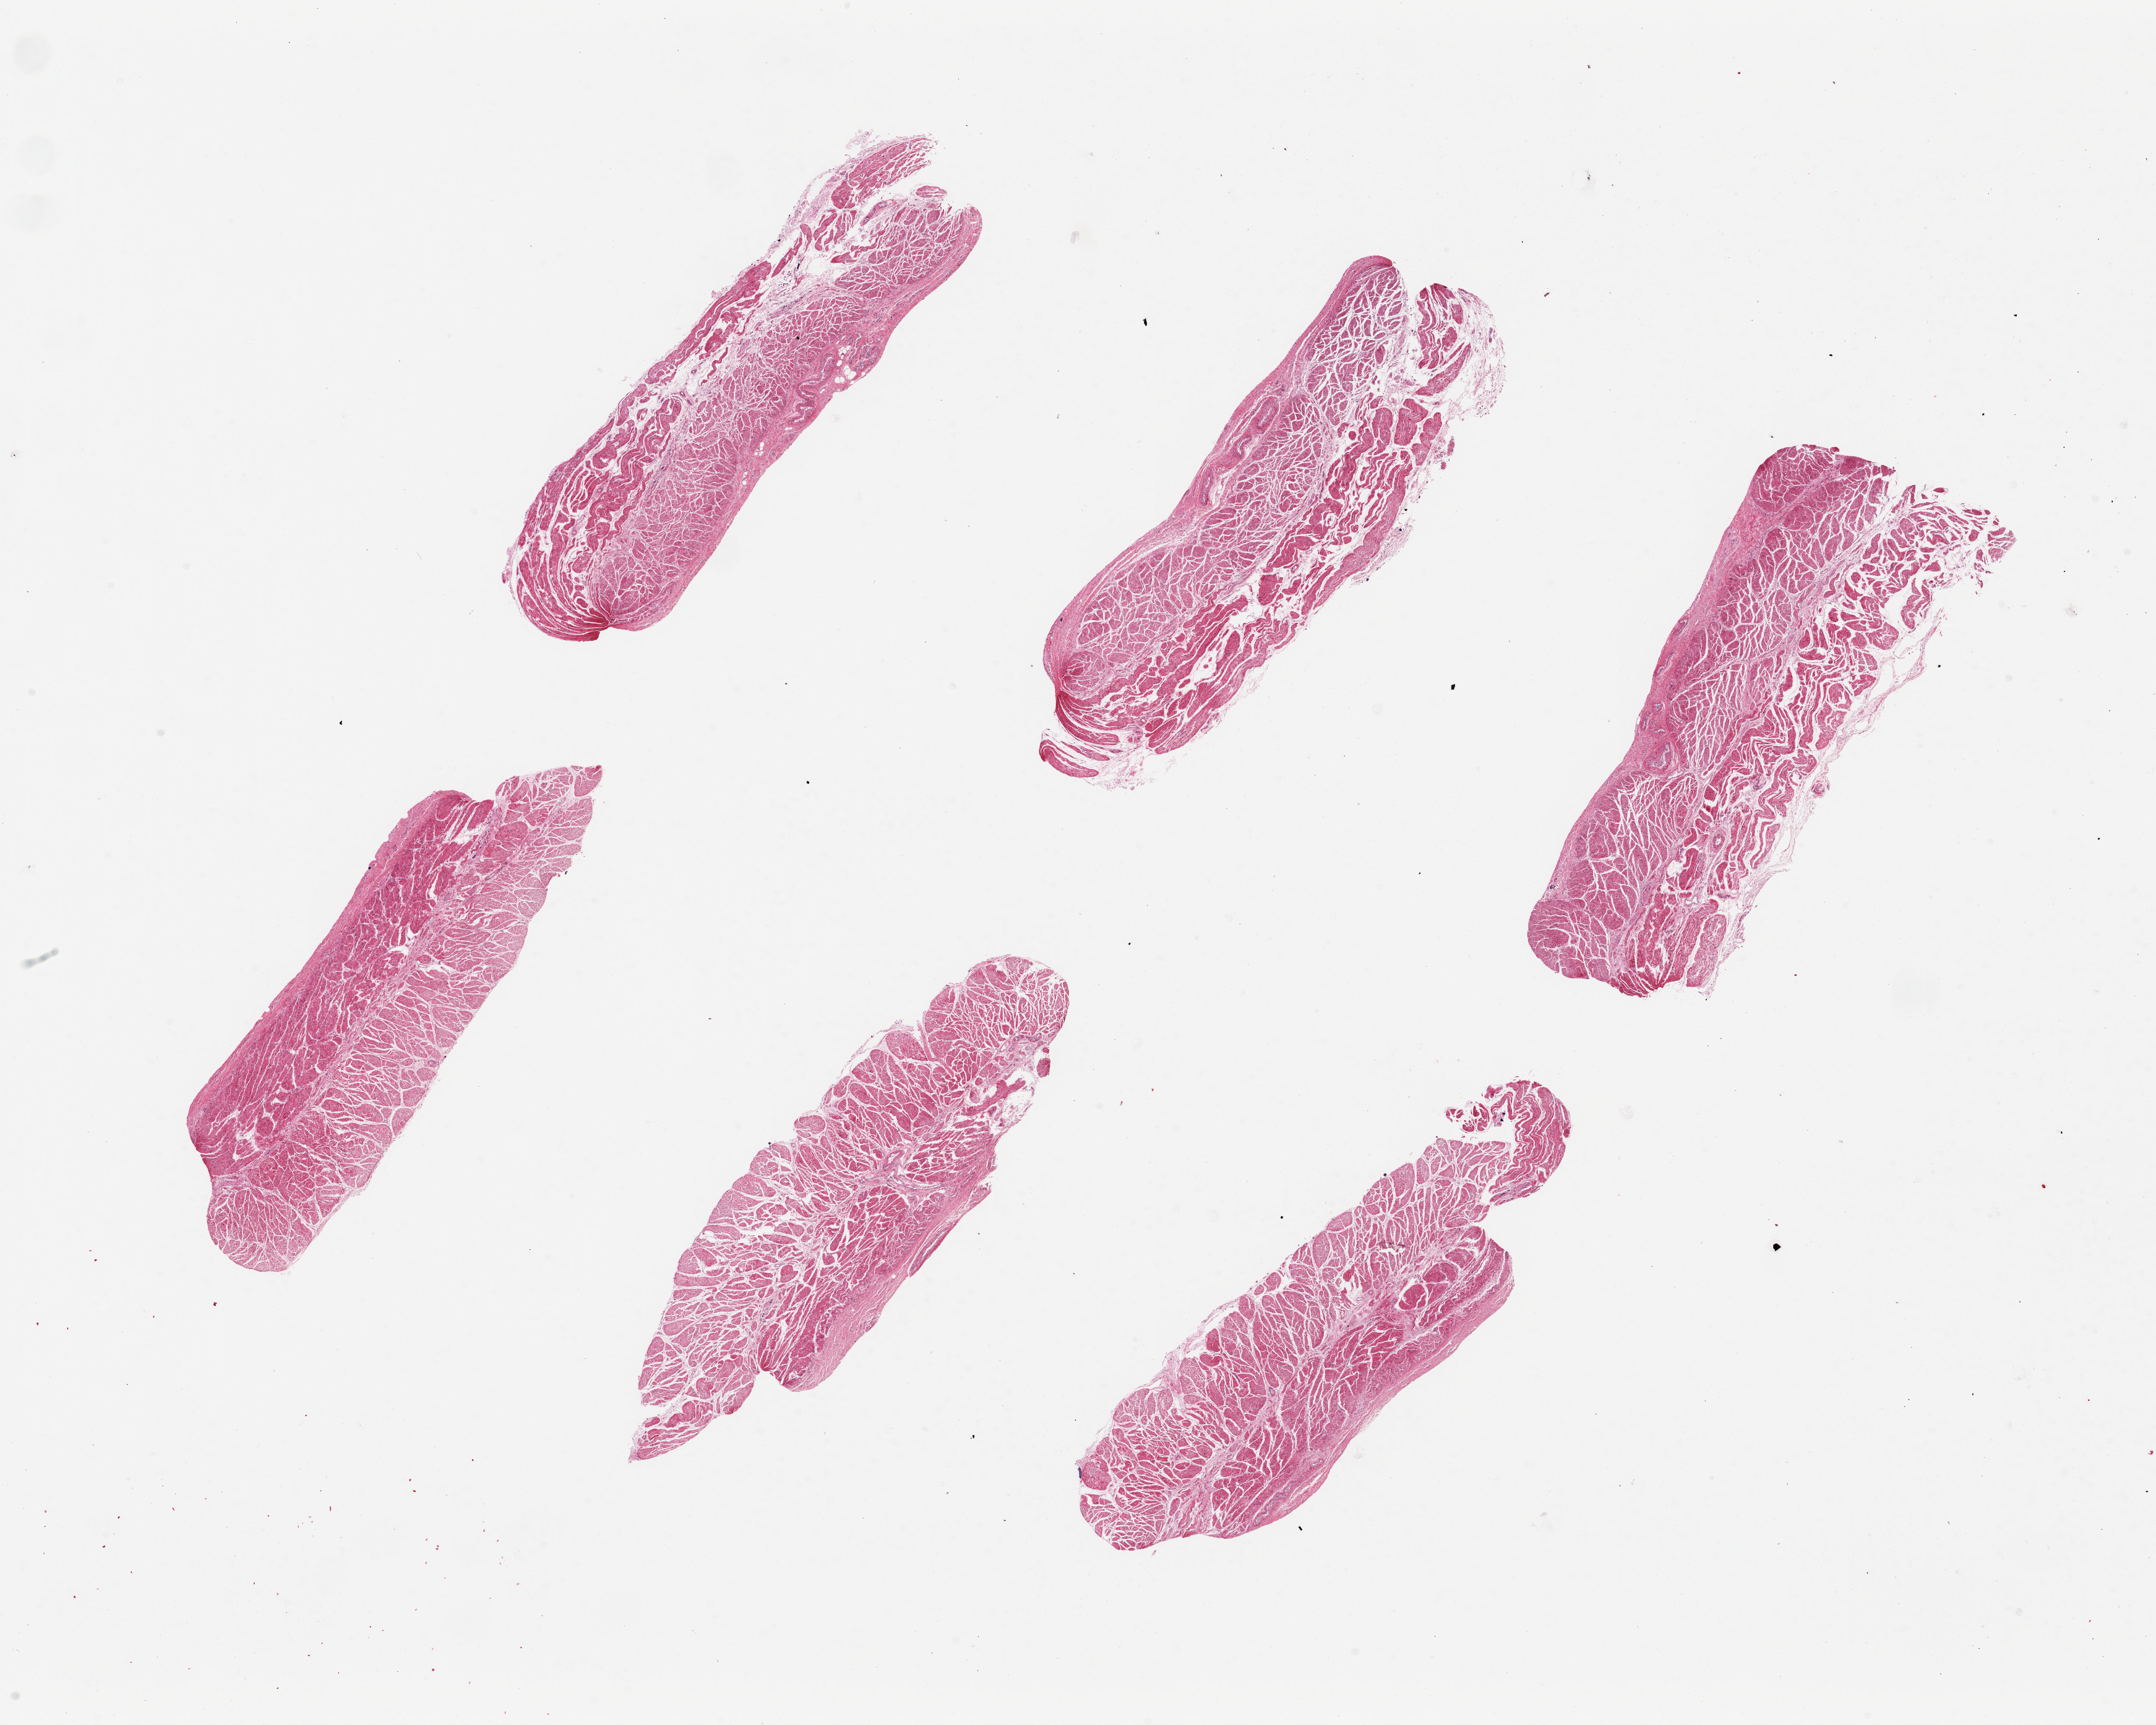
Haematoxylin and eosin whole-slide image, brightfield — whole scanned area (about 27.6 x 22.1 mm, slide scanned at 20x) shown as a low-resolution overview. PAXgene-fixed, paraffin-embedded tissue. Target tissue: esophageal muscle. Donor tissue sample. Donor: male.
Reviewer comment on this tissue sample: 6 pieces, up to 7x3.4mm; 'clean' specimen without extraneous stroma or adipose.